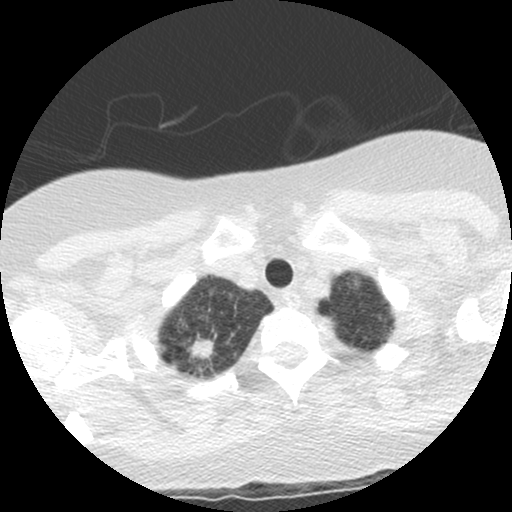
Low-dose screening chest CT, one axial slice. Slice 119 of 130 in the series (ordered by position). Reconstruction kernel STANDARD. Lung window (W 1500 / L -600 HU). 512 × 512 image matrix, field of view 290 × 290 mm.
Outlined on this slice (manually delineated by an expert):
- lesion 1 (tumor, upper lobe of right lung): box from (x=192, y=341) to (x=213, y=358) px